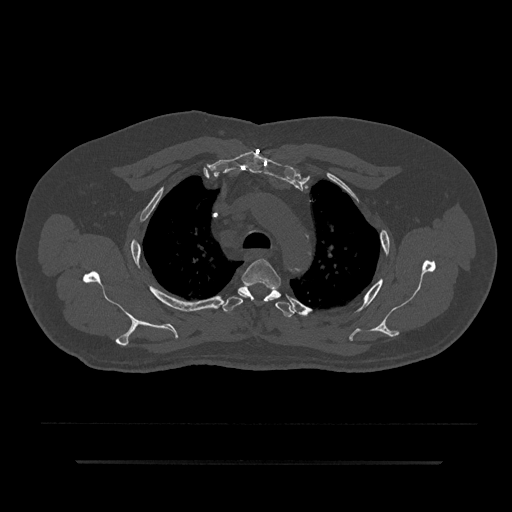
CT including the spine, one axial slice. Slice 639 of 797 in the series (ordered by position). Reconstruction kernel Br40s/3. 120 kVp. Bone window (W 1800 / L 400 HU). 0.5 mm slice thickness. 512 × 512 image matrix, field of view 464 × 464 mm. Patient: male, 59 years. Case-level facts recorded for this patient, not image findings: primary cancer: bile ducts.
Annotated regions visible in this slice (semi-automatic segmentation, software-assisted and operator-edited):
- T3 vertebra: bounding box (x1, y1, x2, y2) in pixels: (241, 258, 281, 288)
- T4 vertebra: (222, 284, 294, 317)